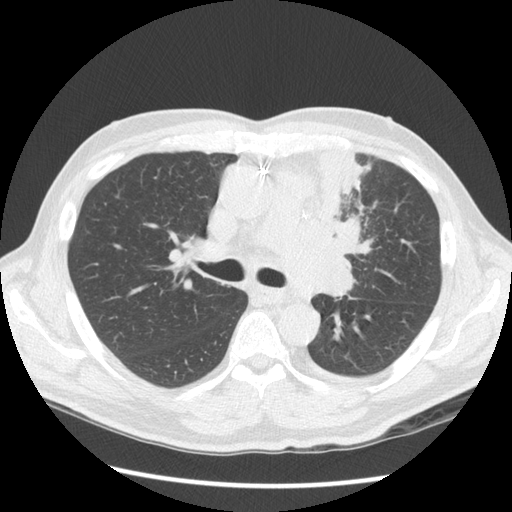
Low-dose screening chest CT, one axial slice. Slice 89 of 136 in the series (ordered by position). Lung window (W 1500 / L -600 HU). 2.5 mm slice thickness. 512 × 512 image matrix, field of view 360 × 360 mm.
Annotated regions visible in this slice (manually delineated by an expert):
- lesion 1 (tumor, upper lobe of left lung): bounding box [x1, y1, x2, y2] px = [301, 150, 374, 298]